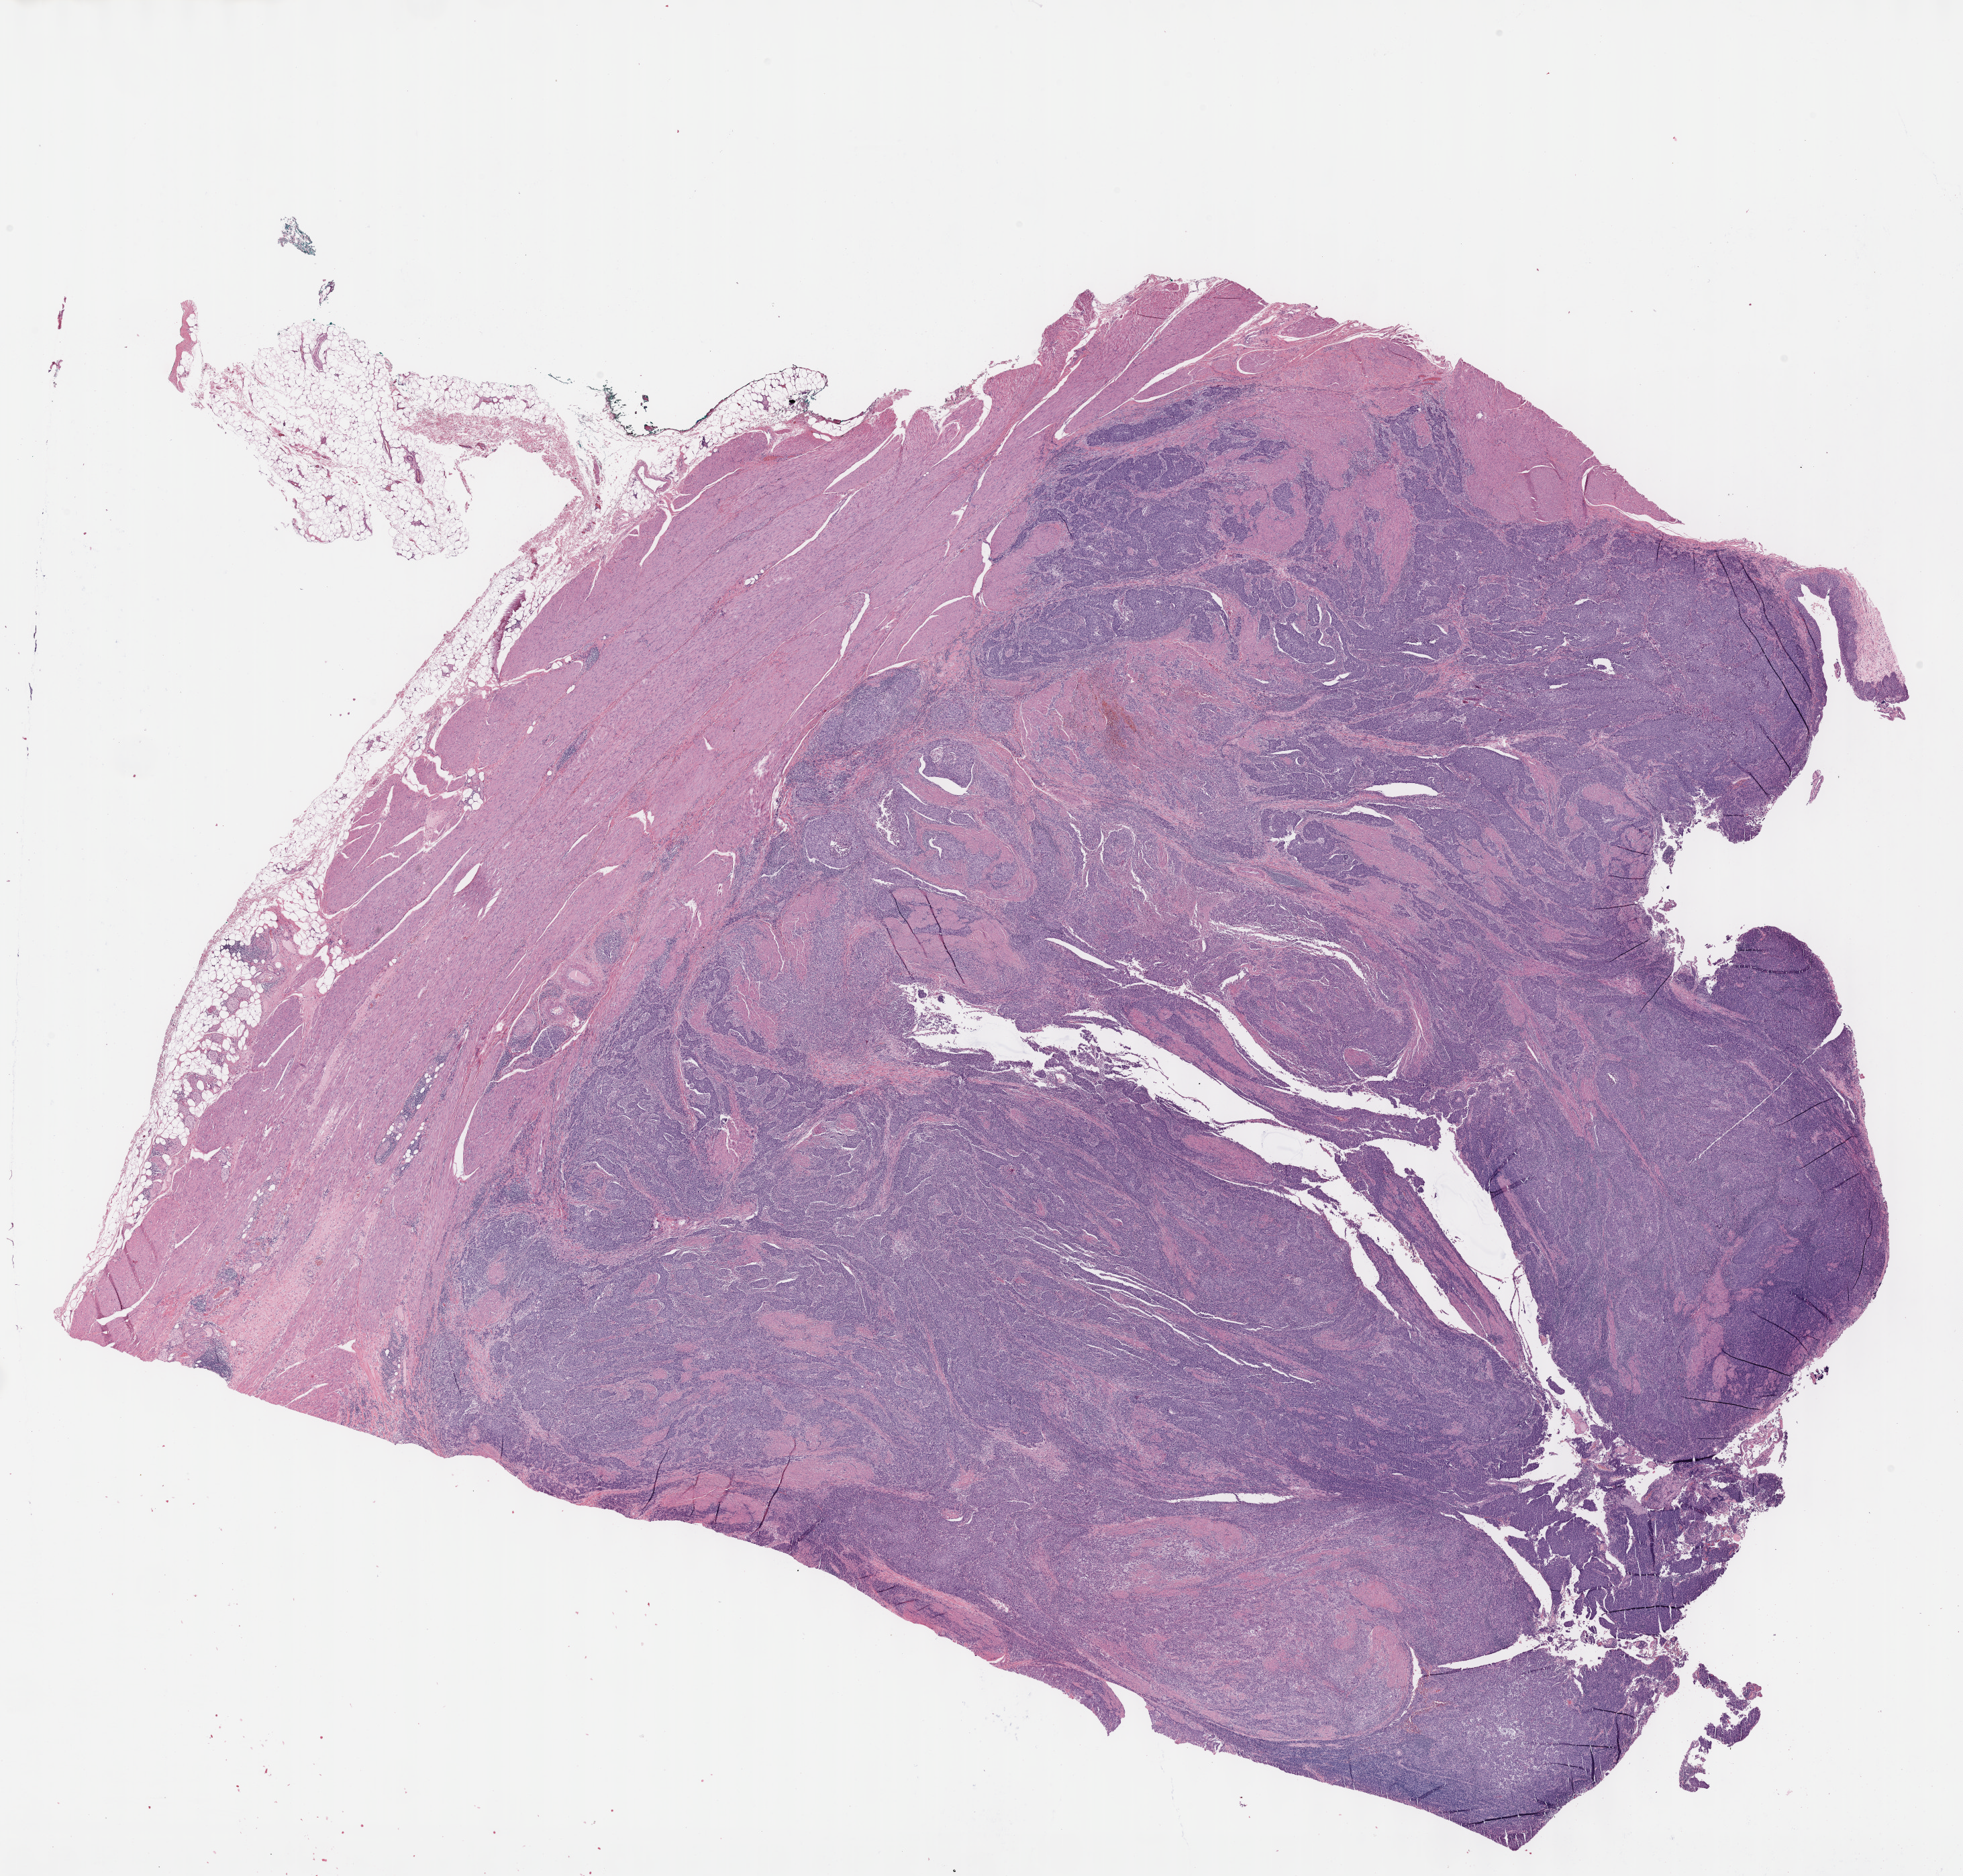
Hematoxylin and eosin (H&E) stained whole-slide image — a low-resolution overview of the entire scanned area, about 23.6 x 22.6 mm (acquisition: 40x scan). FFPE section. Sample: primary tumour, bladder. Patient: male, age at initial diagnosis 79 years. Histologic grade: high grade.
AJCC pathologic stage: III (7th edition). Pathologic diagnosis: Transitional cell carcinoma.